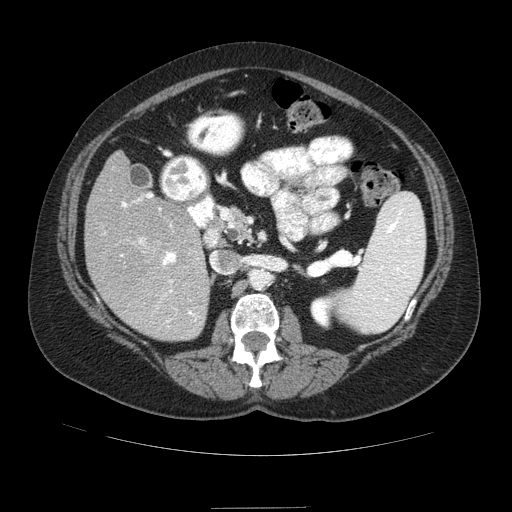
Contrast-enhanced abdominal CT (liver protocol), one axial slice. Slice 38 of 89 in the series (ordered by position). Reconstruction kernel STANDARD. 120 kVp. Soft-tissue window (W 400 / L 40 HU). 2.5 mm slice thickness. 512 × 512 image matrix, field of view 400 × 400 mm. Case-level facts recorded for this patient, not image findings: diagnosis: hepatocellular carcinoma (patient treated with transarterial chemoembolisation; whether this scan precedes or follows treatment is not stated here); TNM stage (as recorded): Stage-IIIB; Child-Pugh class: A; tumour nodularity: multinodular.
Annotated regions visible in this slice (semi-automatically segmented with operator editing):
- liver parenchyma outside the tumour (the mass and vessels are separate outlines, so this box may not span the whole liver): bounding box [x1, y1, x2, y2] px = [84, 152, 210, 340]
- liver vessels: [121, 193, 196, 323]